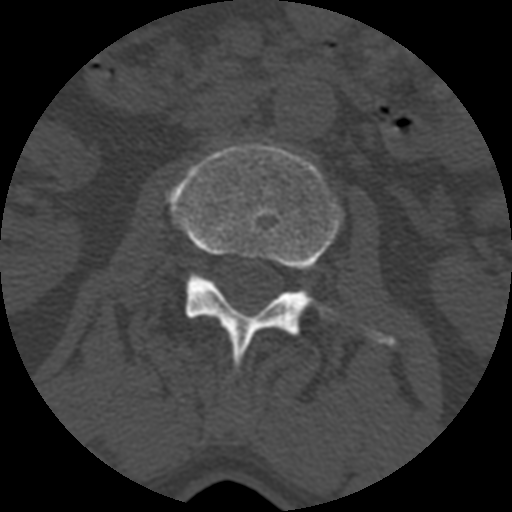
CT including the spine, one axial slice; position 332 of 399 along the scan axis; bone window (W 1800 / L 400 HU); 1.25 mm slice thickness; 512 × 512 image matrix, field of view 160 × 160 mm. Patient age 71 years. From the clinical record (not read from this slice): primary cancer: prostate.
Annotated regions visible in this slice (semi-automatic segmentation, software-assisted and operator-edited):
- L2 vertebra: box from (x=167, y=144) to (x=396, y=371) px